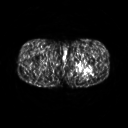
FDG PET of an extremity soft-tissue mass (from a PET/CT study), one axial slice. Slice 246 of 267 in the series (ordered by position). 3.27 mm slice thickness. 128 × 128 image matrix. Patient: male, 27 years. From the clinical record (not read from this slice): histological type: extraskeletal osteosarcoma; grade: high; site of the primary tumour: left adductur.
Annotated regions visible in this slice (expert contour drawn on MRI and transferred to this co-registered scan by the dataset authors):
- gross tumour volume (mass): bounding box [x1, y1, x2, y2] px = [72, 59, 95, 74]